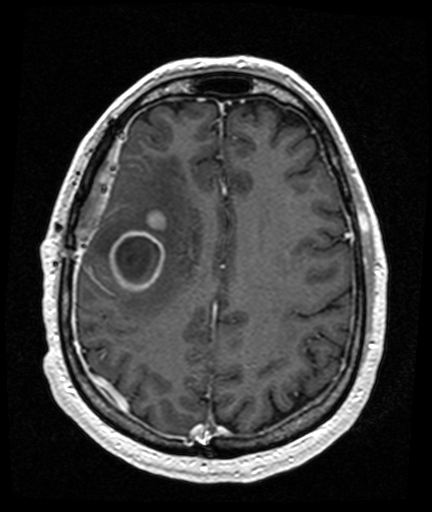
Brain MRI from a brain-tumour surgery series, one axial slice. Position 54 of 176 along the scan axis. T1-weighted post-contrast. 1 mm slice thickness. 432 × 512 image matrix, field of view 194 × 230 mm. From the clinical record (not read from this slice): histopathology: Glioblastoma; WHO grade: 4; IDH mutation: no.
Outlined on this slice (expert manual segmentation):
- tumour: bounding box <111,214,165,291> (left, top, right, bottom; pixels)